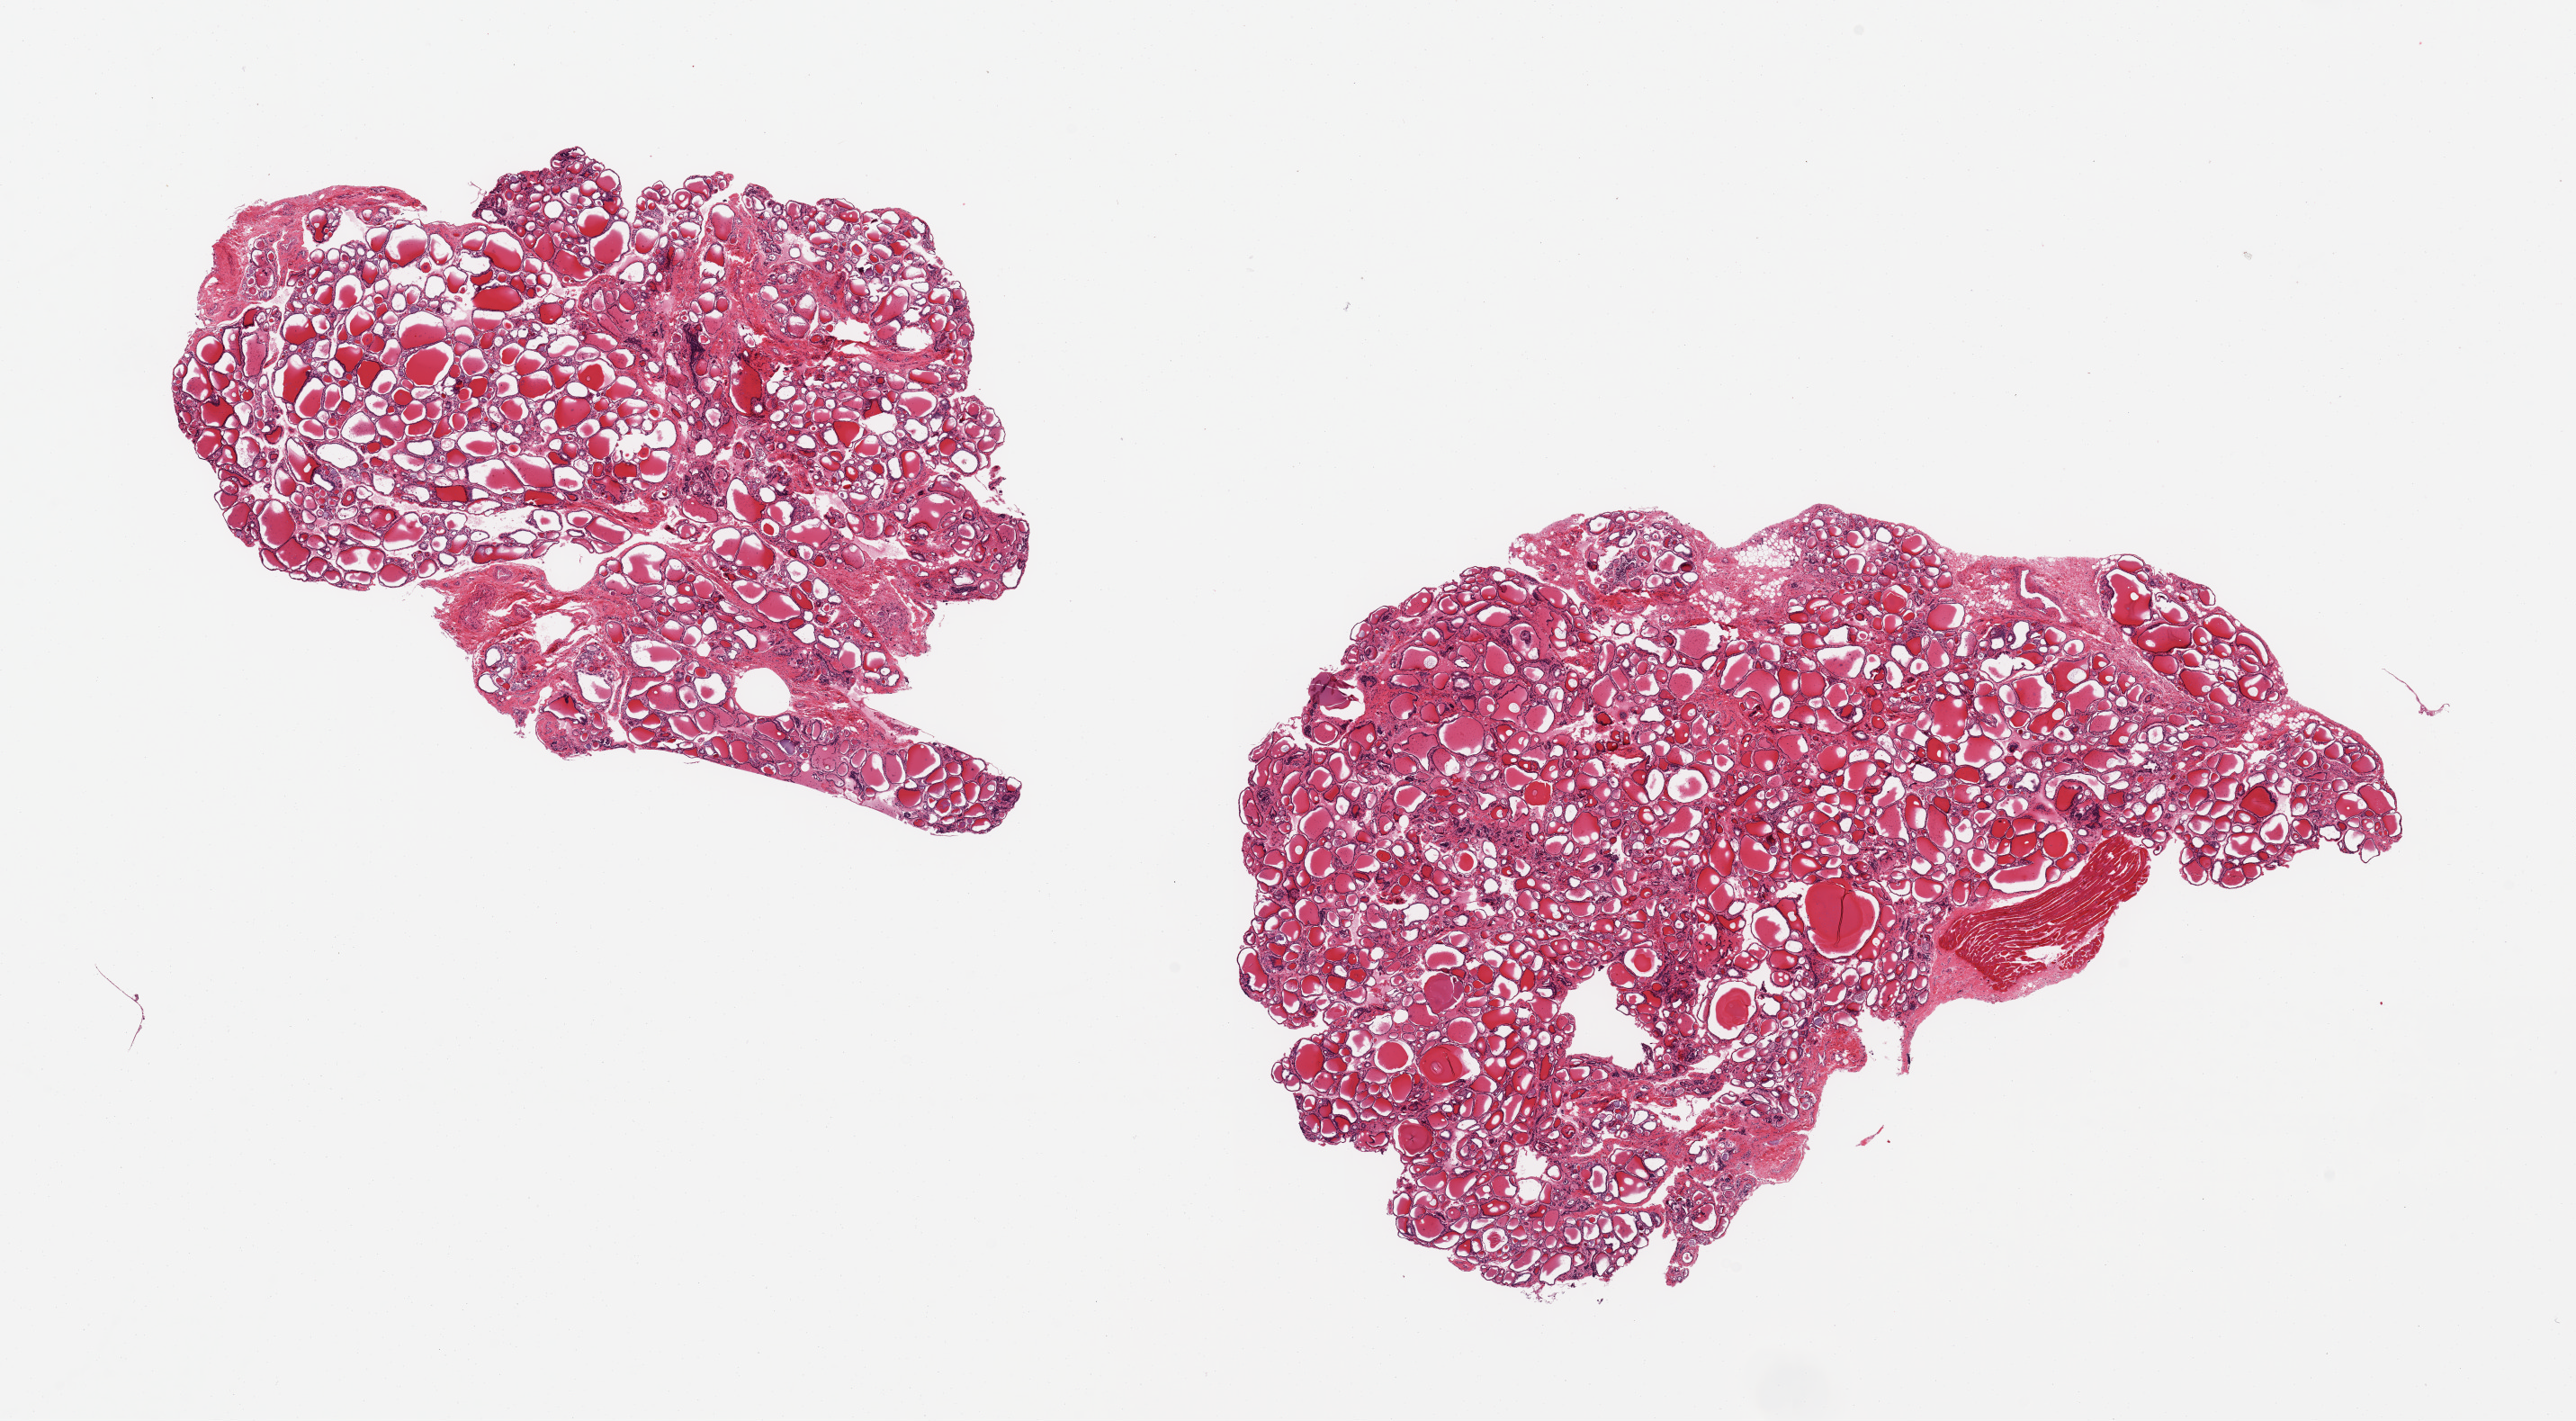
Whole-slide image, H&E stain, shown as a low-resolution overview of the whole scanned area (about 22.6 x 12.5 mm, acquisition: 20x scan). PAXgene-fixed paraffin-embedded (PFPE) section. Section of thyroid (target tissue). Tissue donor sample. Male donor.
Reviewer comment on this tissue sample: 2 pieces, 9x6 & 8x5mm.